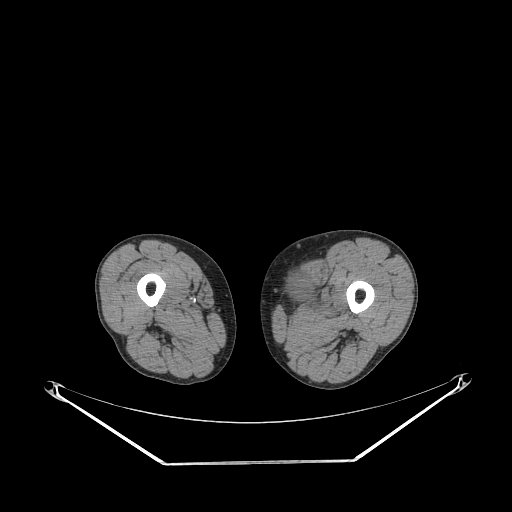
CT of an extremity soft-tissue mass (from a PET/CT study), one axial slice; slice 225 of 267 in the series (ordered by position); 140 kVp; soft-tissue window (W 400 / L 40 HU); 3.75 mm slice thickness; 512 × 512 image matrix. Male patient. Case-level facts recorded for this patient, not image findings: histological type: pleiomorphic liposarcoma; grade: high; site of the primary tumour: left thigh.
Structures marked on this image (expert contour drawn on MRI and transferred to this co-registered scan by the dataset authors):
- gross tumour volume including surrounding oedema: bounding box [x1, y1, x2, y2] px = [290, 272, 337, 314]
- gross tumour volume (mass): [290, 272, 312, 296]